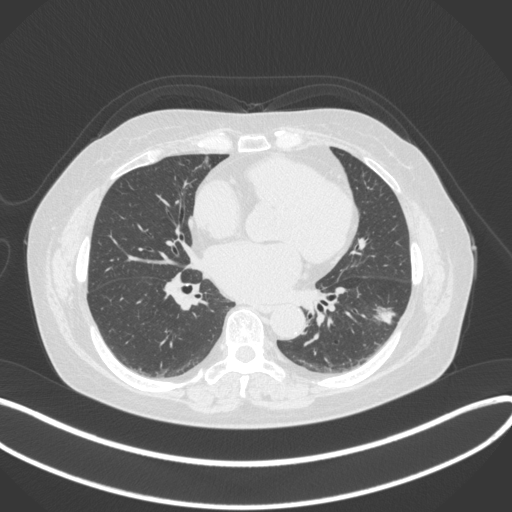
Chest CT, one axial slice; slice 162 of 373 in the series (ordered by position); reconstruction kernel B31f; lung window (W 1500 / L -600 HU); 512 × 512 image matrix, field of view 400 × 400 mm. Female patient, age 67 years. From the clinical record (not read from this slice): clinical TNM (as recorded): T1c N0 M0; histopathological grade: G2.
Structures marked on this image (rectangle marked by the reading radiologist):
- lung tumour (recorded histology: adenocarcinoma): box from (x=365, y=299) to (x=401, y=328) px